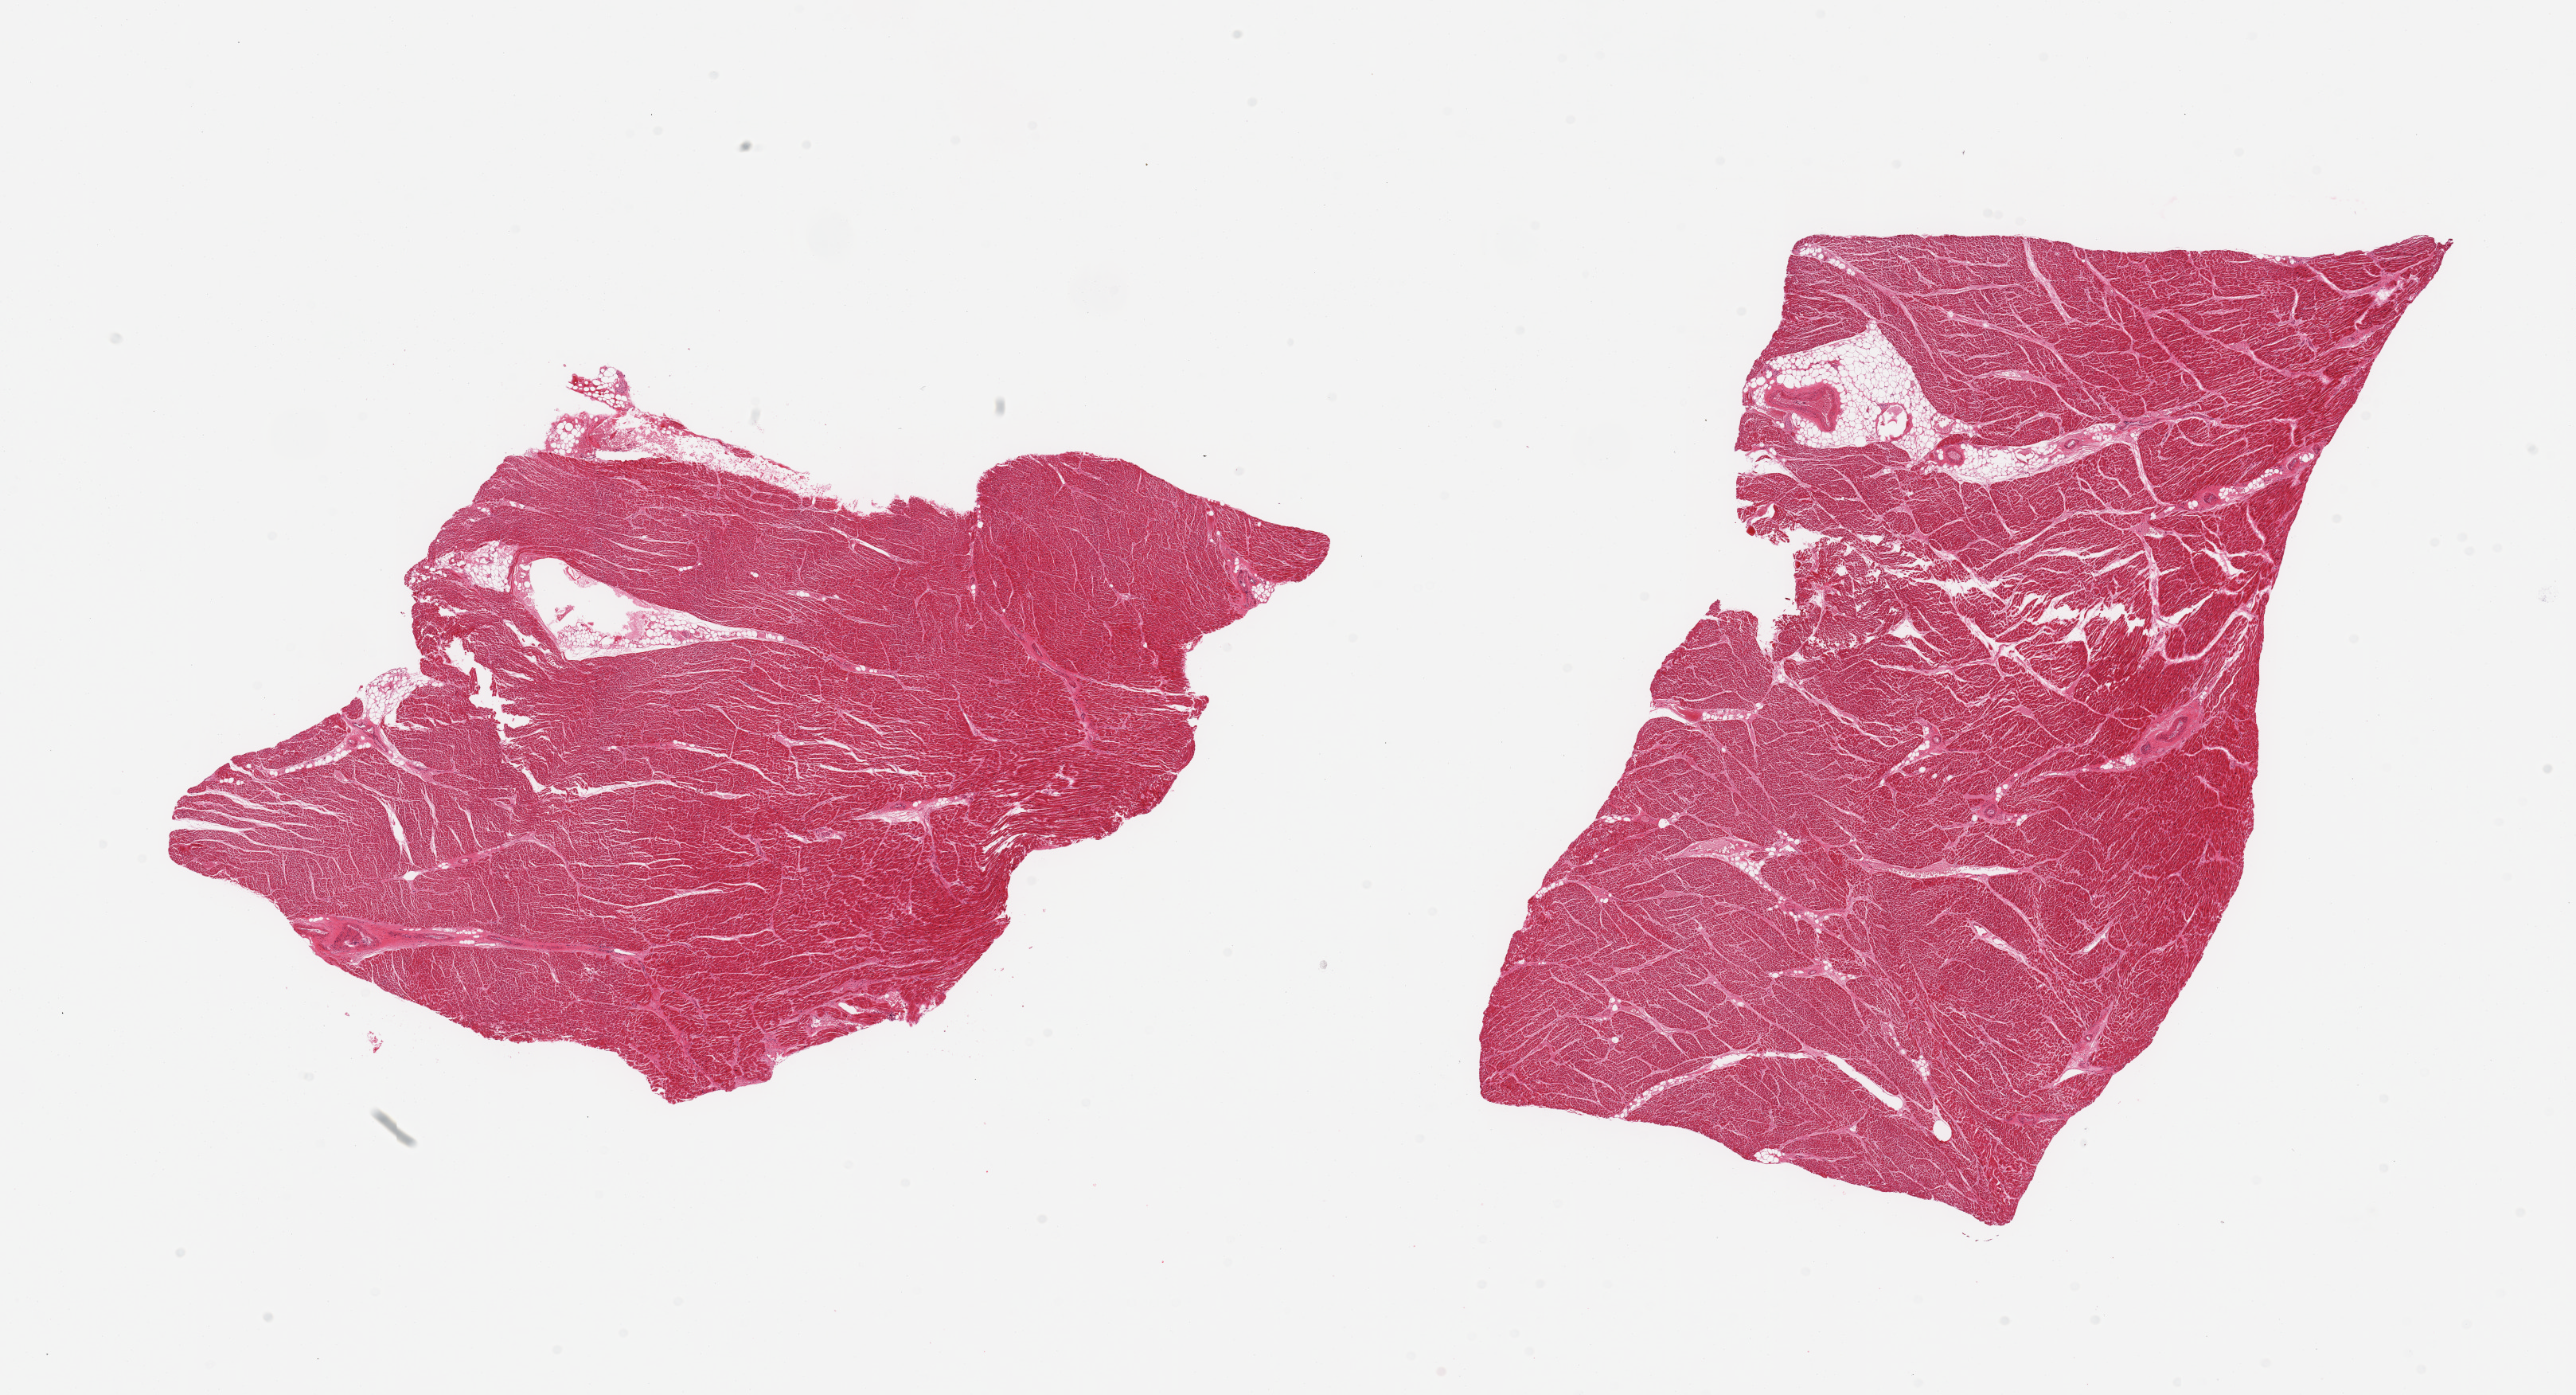
H&E whole-slide image, brightfield, a low-resolution overview of the entire scanned area, about 25.6 x 13.9 mm (slide scanned at 20x); PAXgene-fixed paraffin-embedded (PFPE) section; sampled site (target tissue): heart; donor tissue sample. Donor: male.
• pathologist's review note for this sample: 2 pieces, mild/moderate interstitial fibrosis/chronic ischemic changes